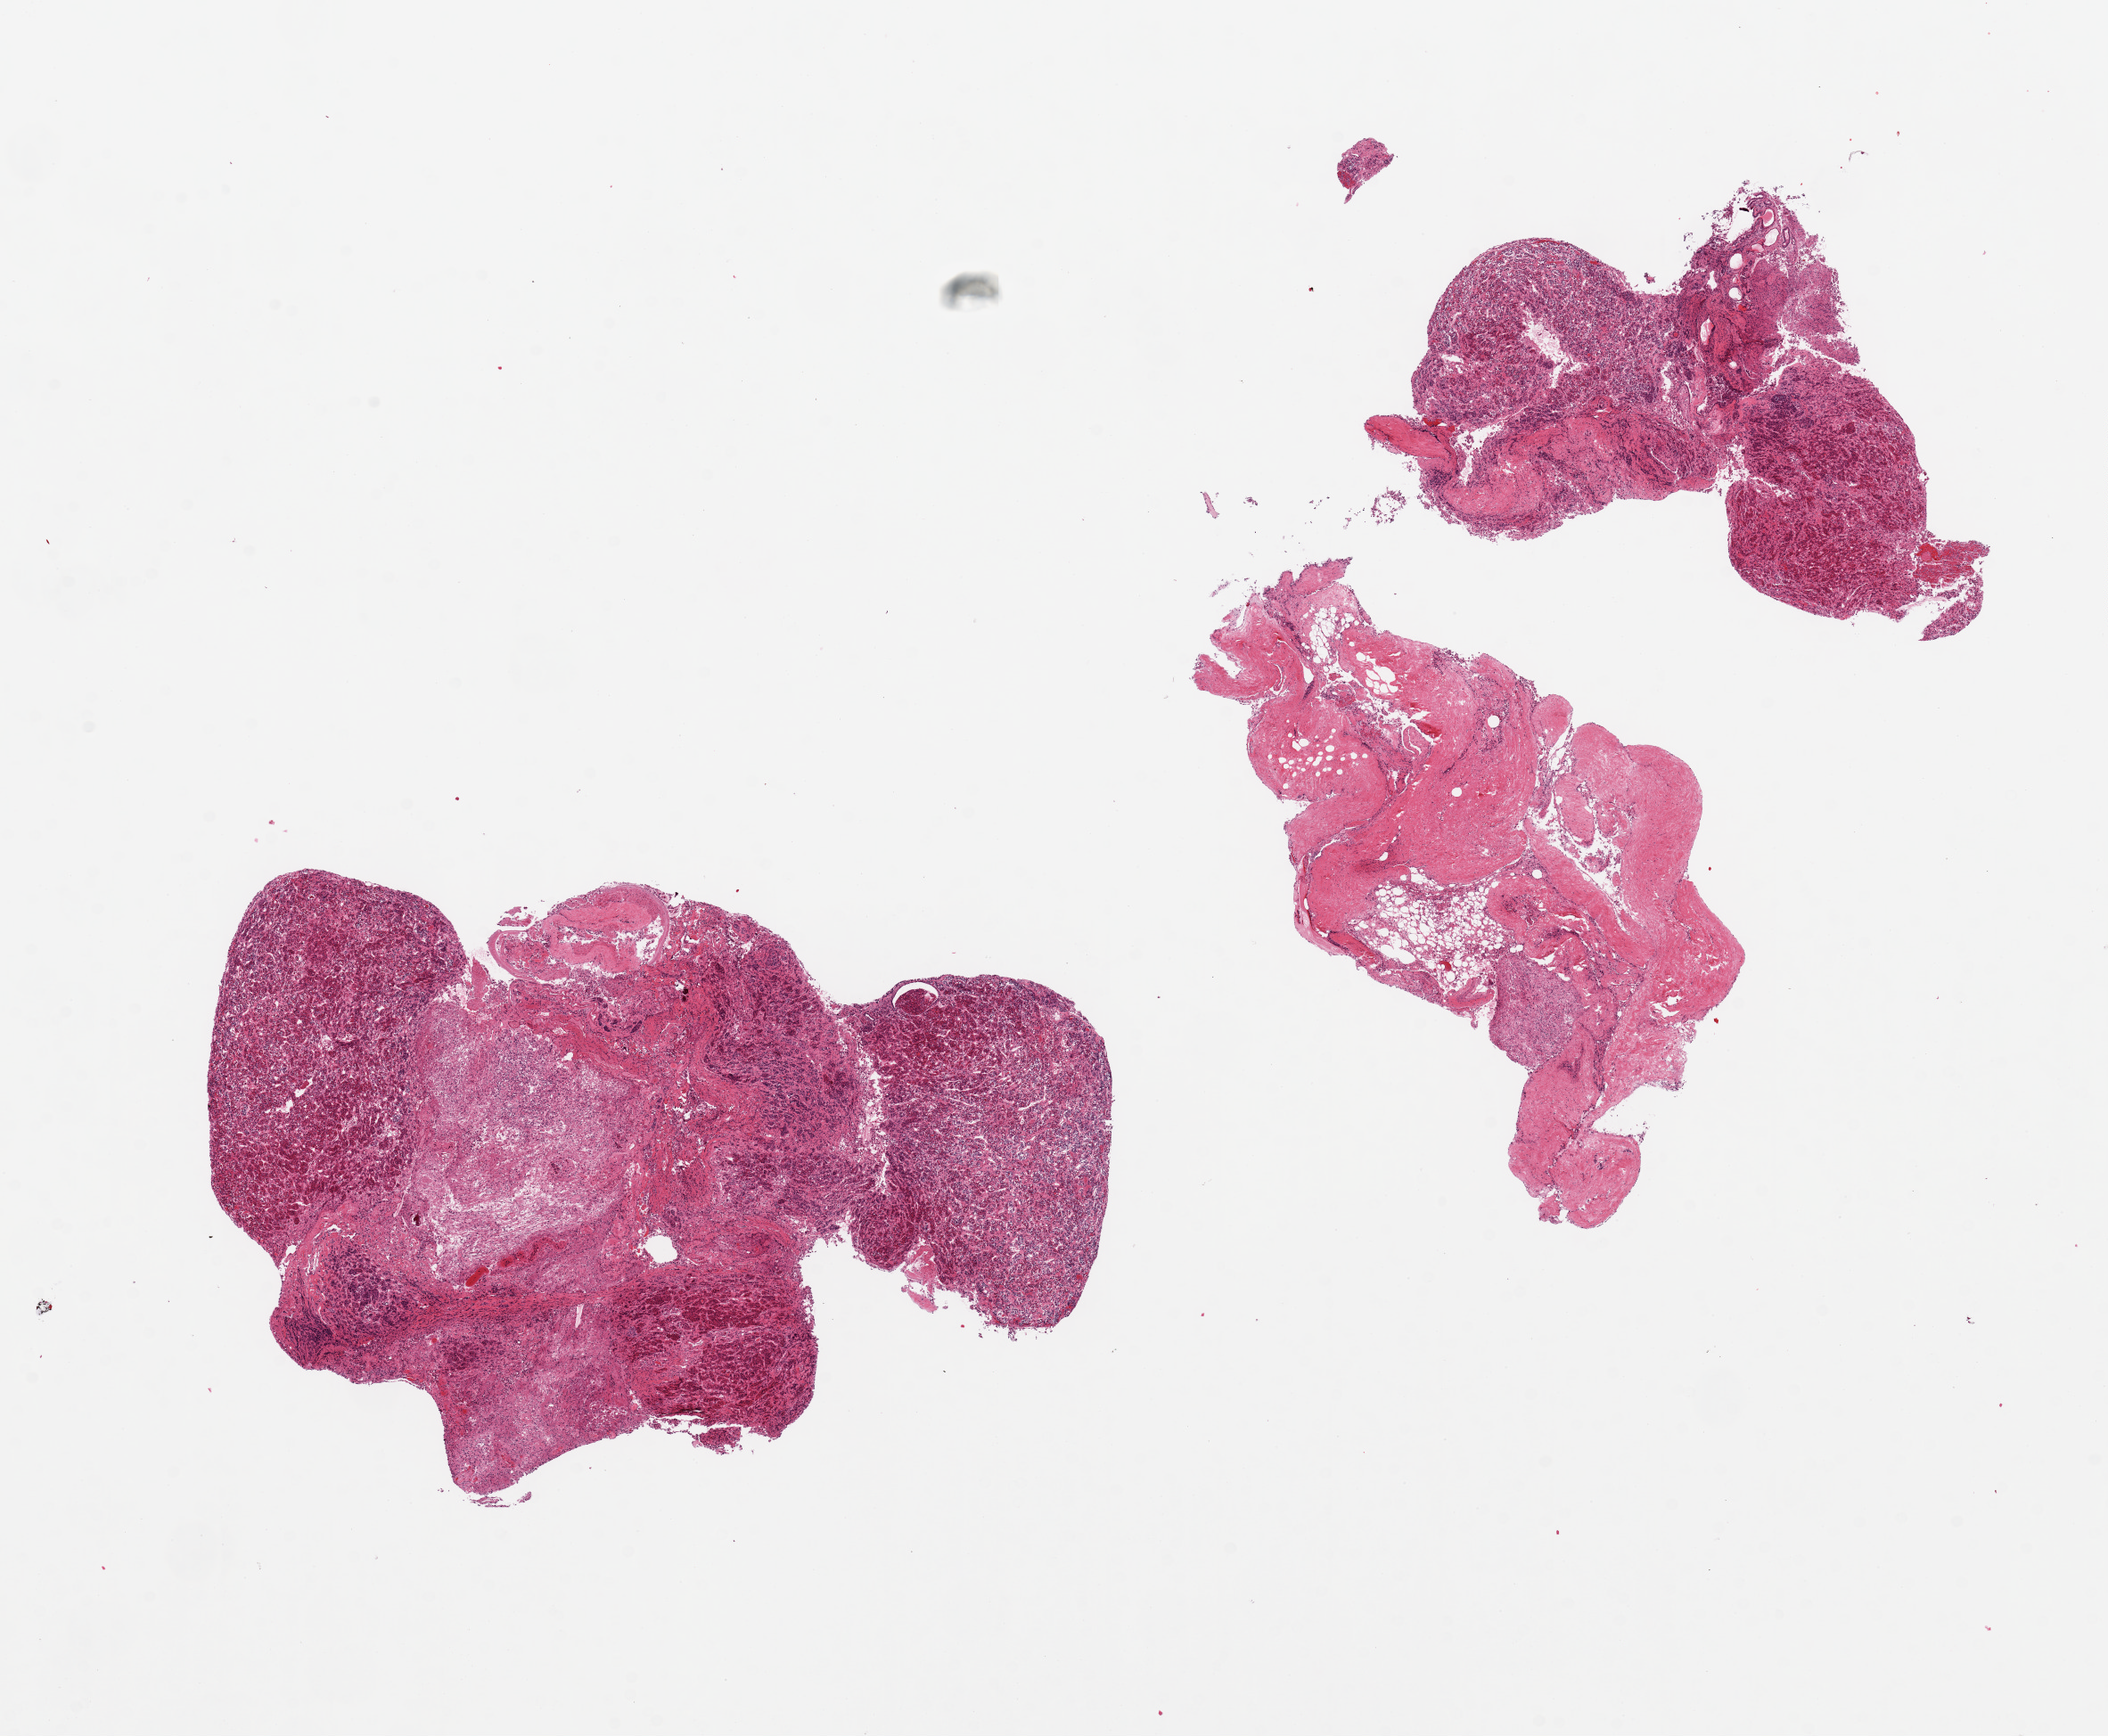
Digitized hematoxylin and eosin (H&E)-stained section, a low-resolution overview of the entire scanned area, about 18.7 x 15.4 mm (from a 20x scan); PAXgene-fixed, paraffin-embedded tissue; section of pituitary (target tissue); tissue donor sample.
Reviewer comment on this tissue sample: 2 pieces gland + 1 piece dura; ~40% neurohypophysis, rest adenohypophysis, but badly autolyzed.